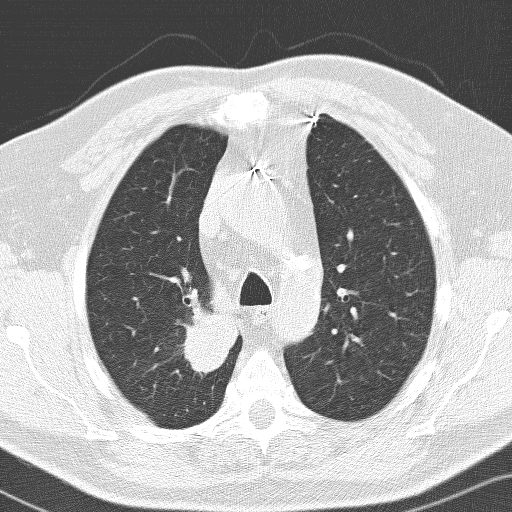
Low-dose screening chest CT, axial slice. Baseline screening round. Lung window (W 1500 / L -600 HU). 120 kVp. Slice 35 of 141 in the series. 512 × 512 image matrix. Male participant, aged 66 years at enrolment. Former smoker at enrolment.
Expert-annotated lung lesion, bounding box [x1, y1, x2, y2] px = [149, 303, 232, 392]. The exam's reader record, not a measurement of the box and not confirmed to be the same lesion: non-calcified nodule or mass ≥4 mm, right upper lobe, 36 × 30 mm, spiculated (stellate) margins, soft tissue attenuation. Official screen result: positive, change unspecified: nodule(s) >= 4 mm or enlarging nodule(s), mass(es), or other non-specific abnormalities suspicious for lung cancer.